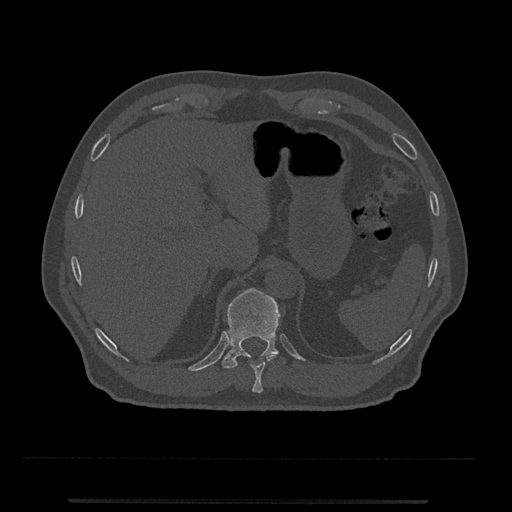
CT including the spine, one axial slice. Slice 485 of 797 in the series (ordered by position). Reconstruction kernel Br40s/3. Bone window (W 1800 / L 400 HU). 0.5 mm slice thickness. 512 × 512 image matrix. Patient: male, 63 years. From the clinical record (not read from this slice): primary cancer: prostate.
Structures marked on this image (semi-automatically segmented with operator editing):
- T10 vertebra: bounding box <250,354,277,393> (left, top, right, bottom; pixels)
- T11 vertebra: <222,288,280,369>